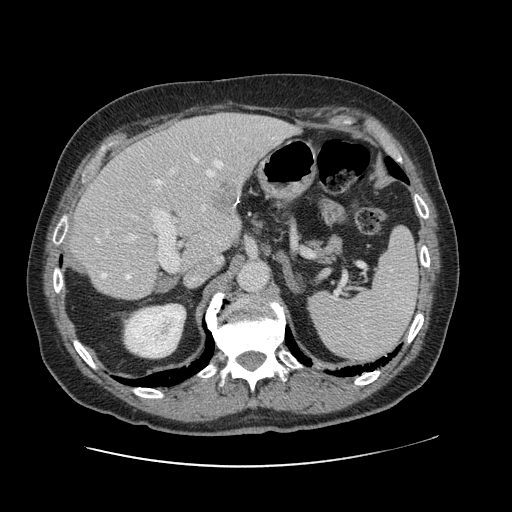
Contrast-enhanced abdominal CT, one axial slice. Position 73 of 138 along the scan axis. Intravenous contrast given. Soft-tissue window (W 400 / L 40 HU). 2.5 mm slice thickness. 512 × 512 image matrix. Male patient, age 71 years. Case-level facts recorded for this patient, not image findings: diagnosis: colorectal cancer liver metastases, imaged before liver resection; multiple liver metastases: no; largest metastasis: 3.3 cm; disease in both lobes: no.
Annotated regions visible in this slice (outlined manually by an expert reader):
- hepatic veins: bounding box <96,158,238,279> (left, top, right, bottom; pixels)
- liver: <71,114,292,300>
- planned liver remnant (the part of the liver to remain after resection): <71,148,228,300>
- portal vein (with intrahepatic branches): <119,168,179,271>
- liver metastasis: <208,183,237,217>